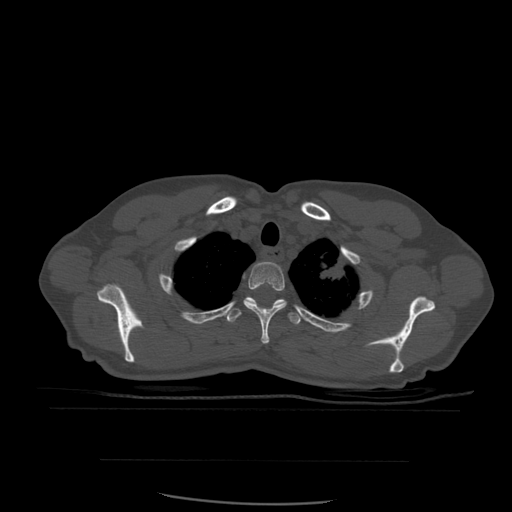
CT including the spine, one axial slice. Slice 453 of 574 in the series (ordered by position). Bone window (W 1800 / L 400 HU). 1.25 mm slice thickness. 512 × 512 image matrix. Patient age 48 years. Case-level facts recorded for this patient, not image findings: primary cancer: lung; vertebrae with lytic lesions (as recorded): T11.
Annotated regions visible in this slice (semi-automatic segmentation, software-assisted and operator-edited):
- T2 vertebra: bounding box <244,262,287,344> (left, top, right, bottom; pixels)
- T3 vertebra: <225,297,303,326>